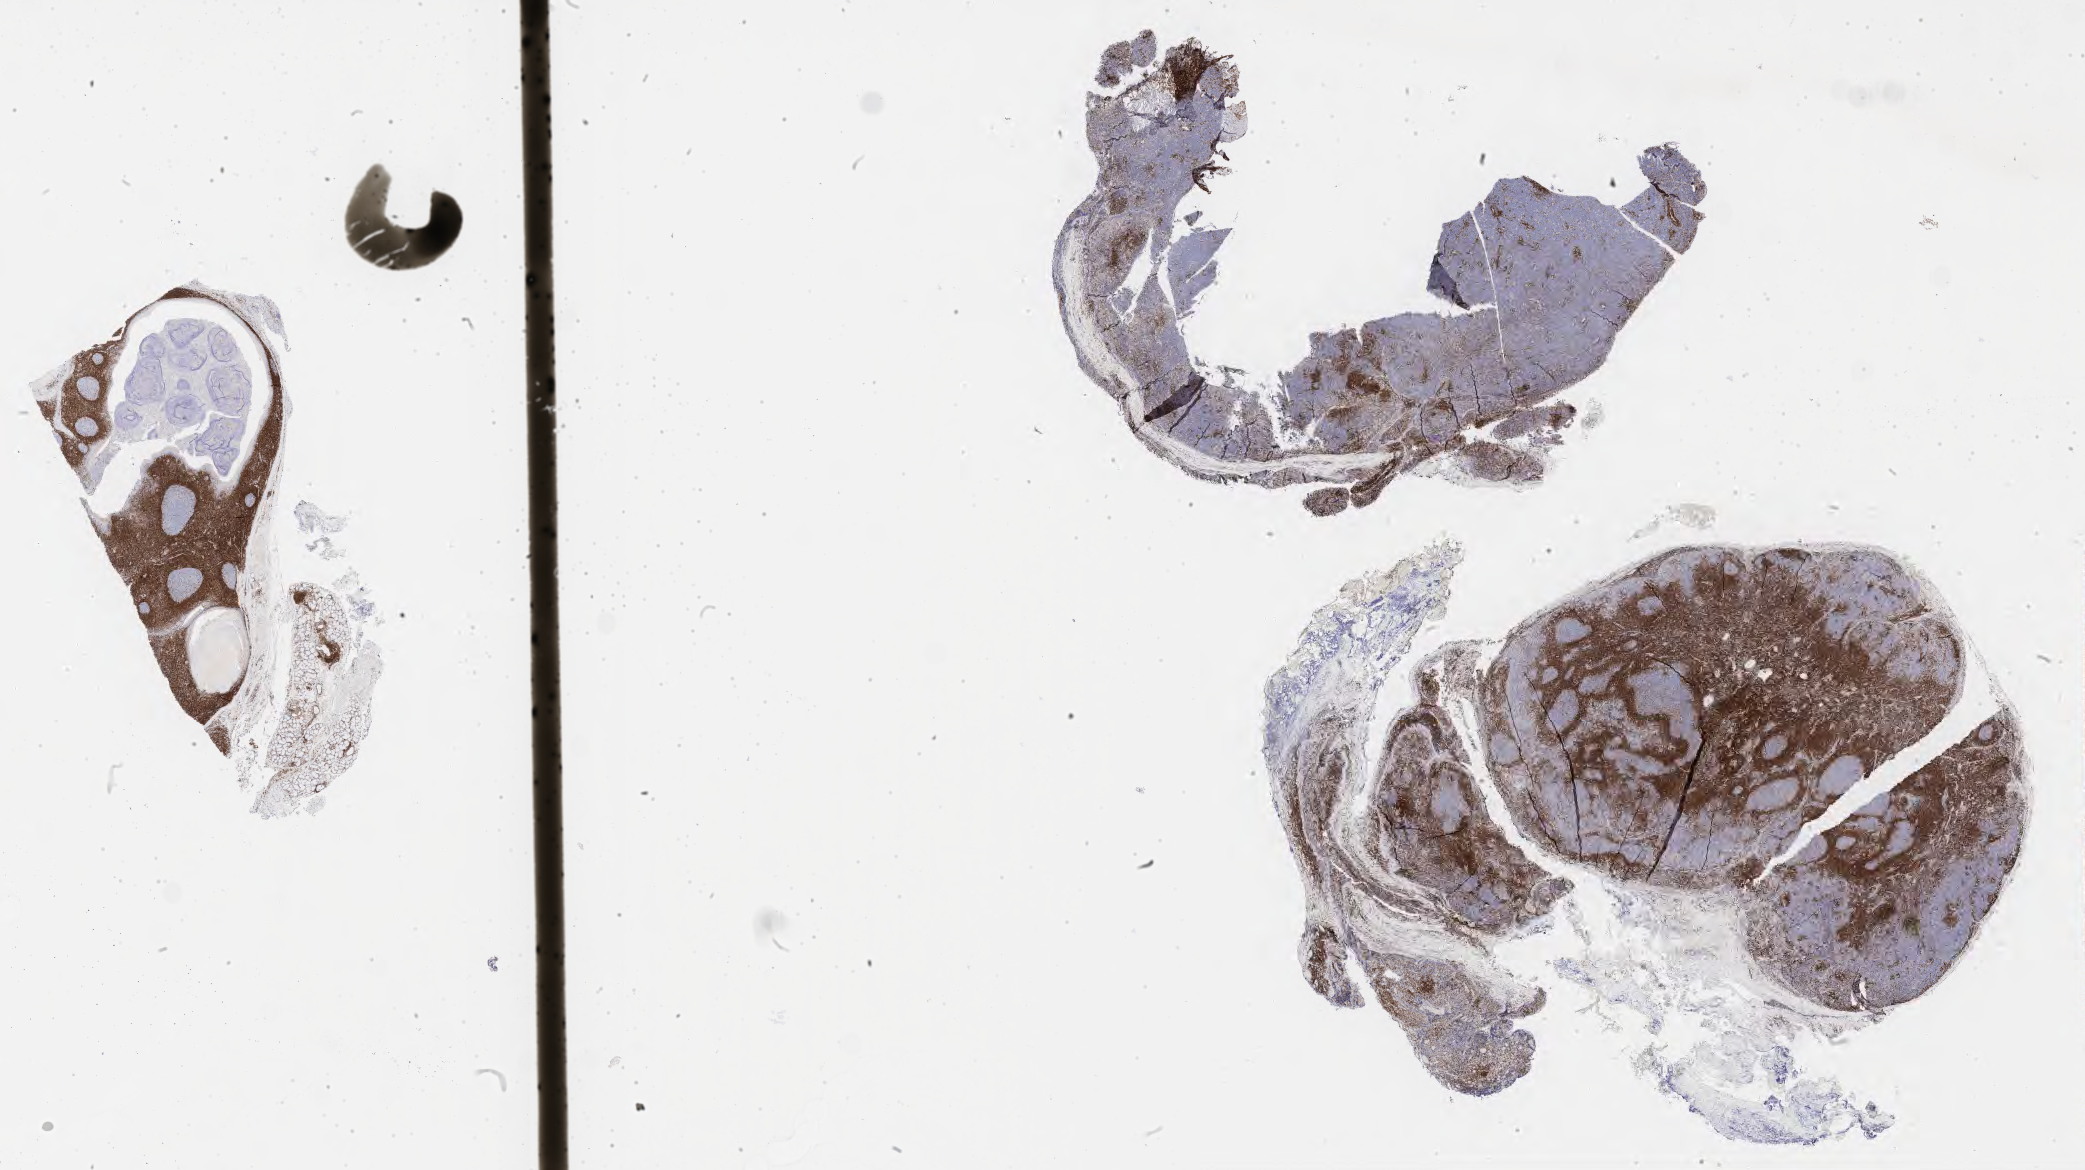
IHC for BCL2, whole-slide image, low-resolution overview of the scanned area, about 33.7 x 18.9 mm. Tumor tissue. Patient: male, 25 years old.
* diagnosis: Burkitt lymphoma, NOS